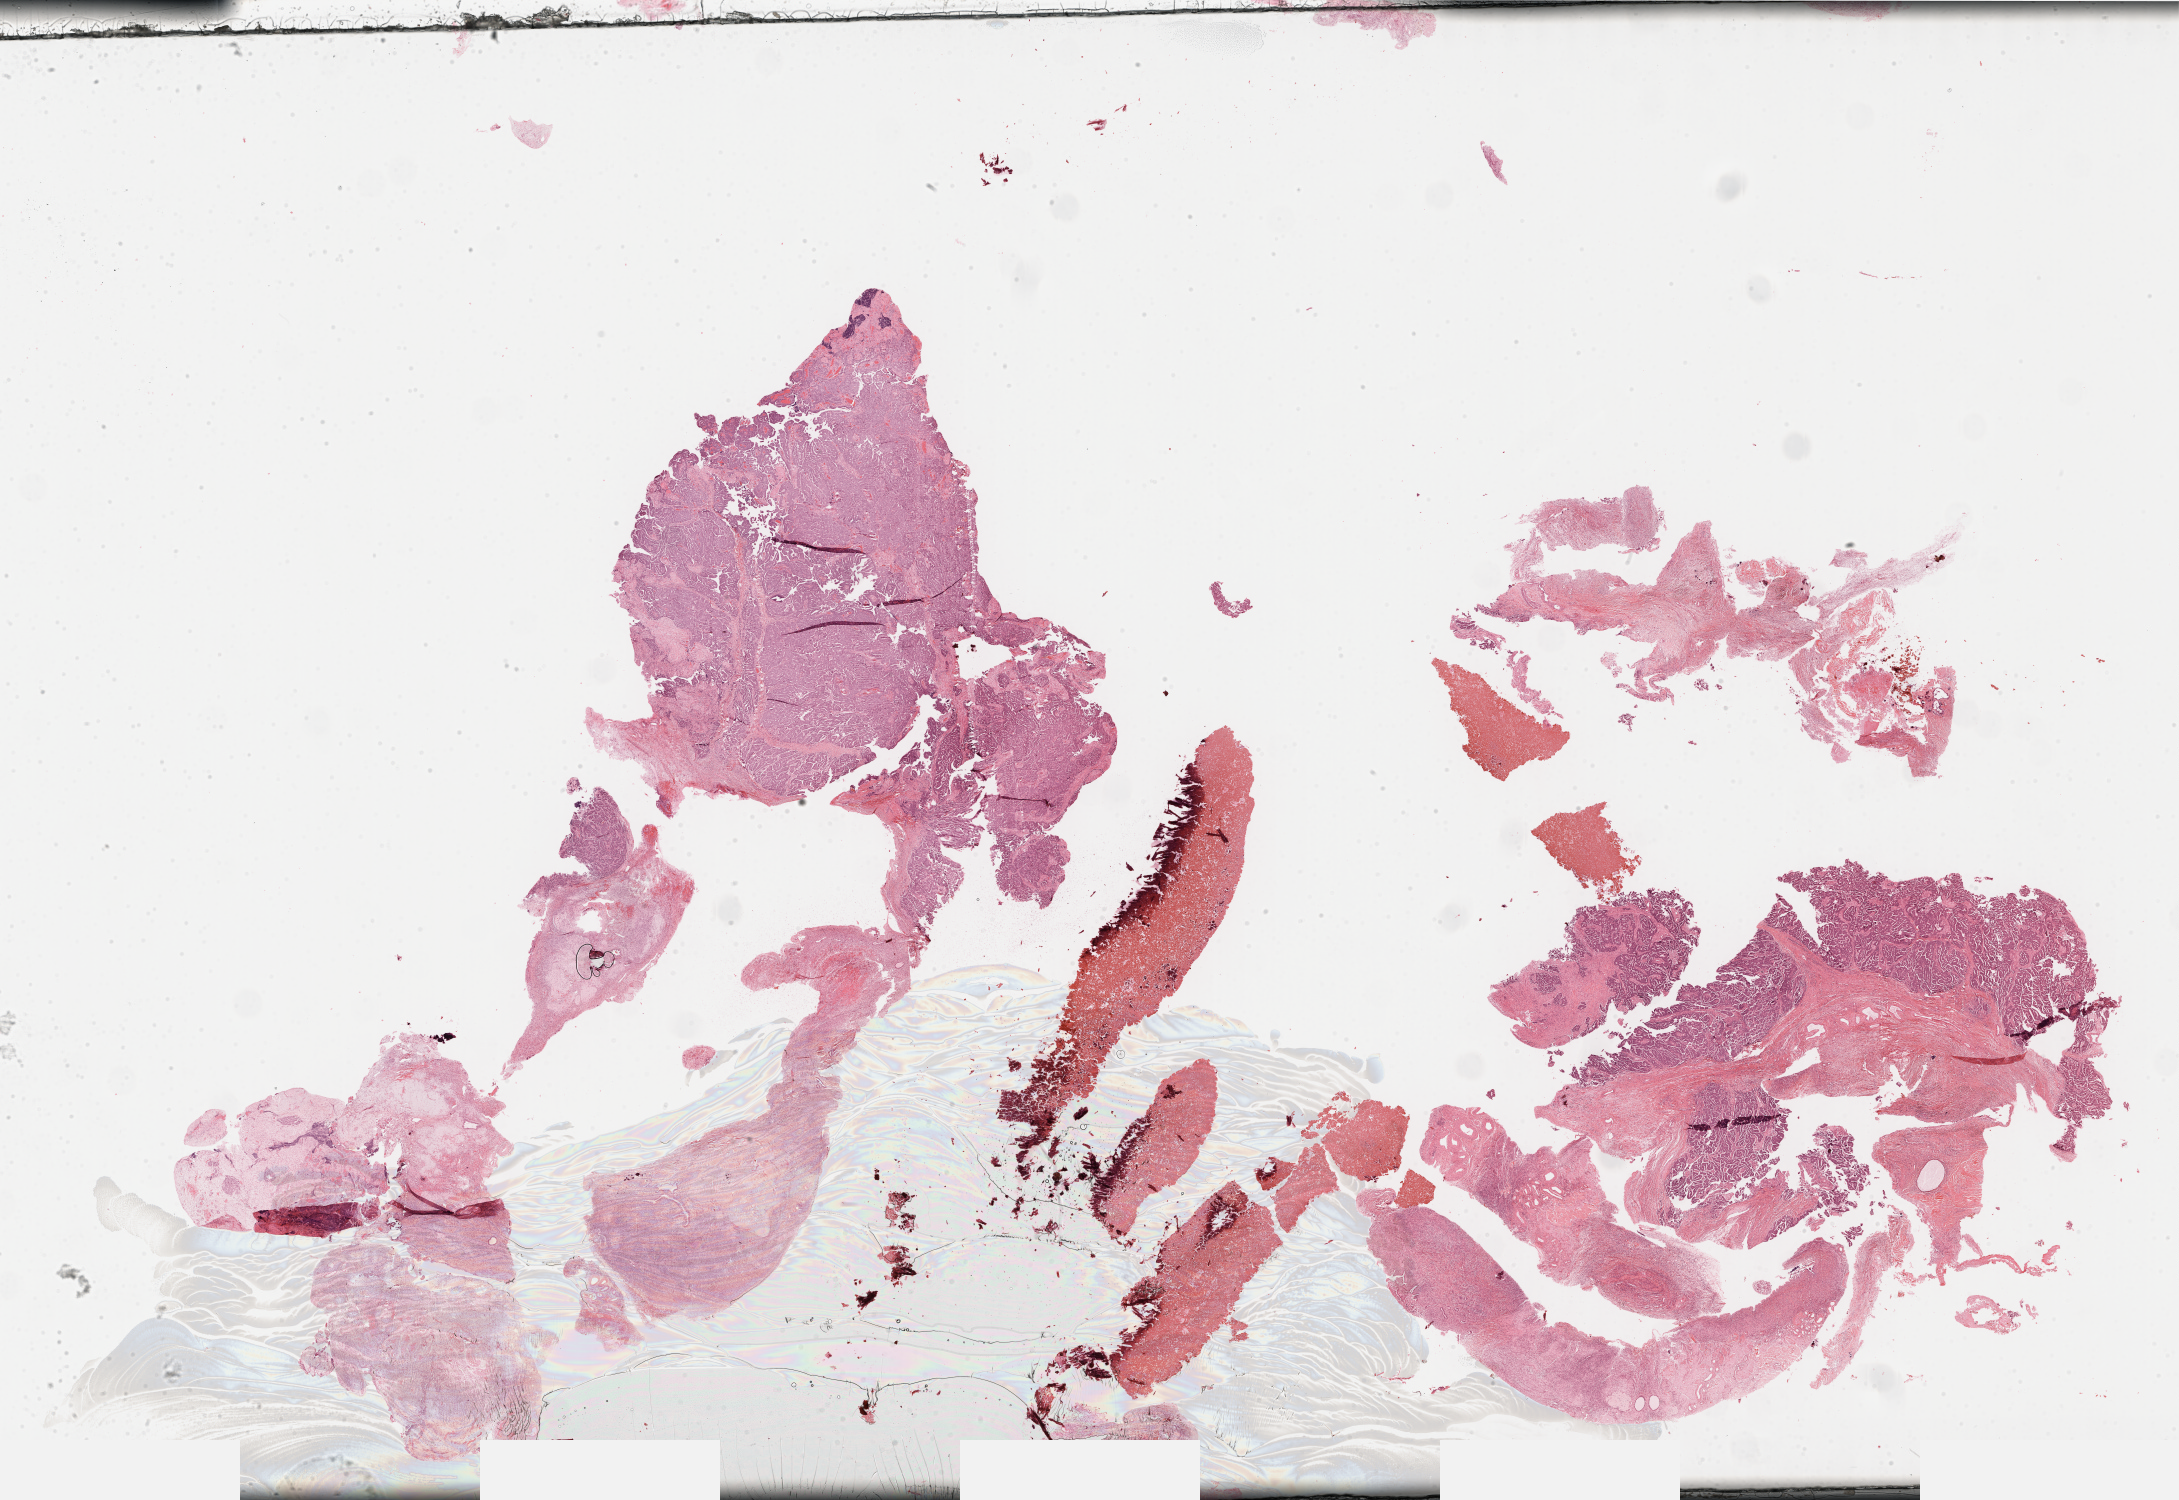
Hematoxylin and eosin (H&E) stained whole-slide image — low-resolution overview of the scanned area, about 35.2 x 24.2 mm; FFPE section; sample: primary tumour, ovary. Female patient; age at initial diagnosis 71 years. Histologic grade: G3 (poorly differentiated).
* FIGO stage: IIIC
* laterality: bilateral
* histologic diagnosis: Serous cystadenocarcinoma, NOS